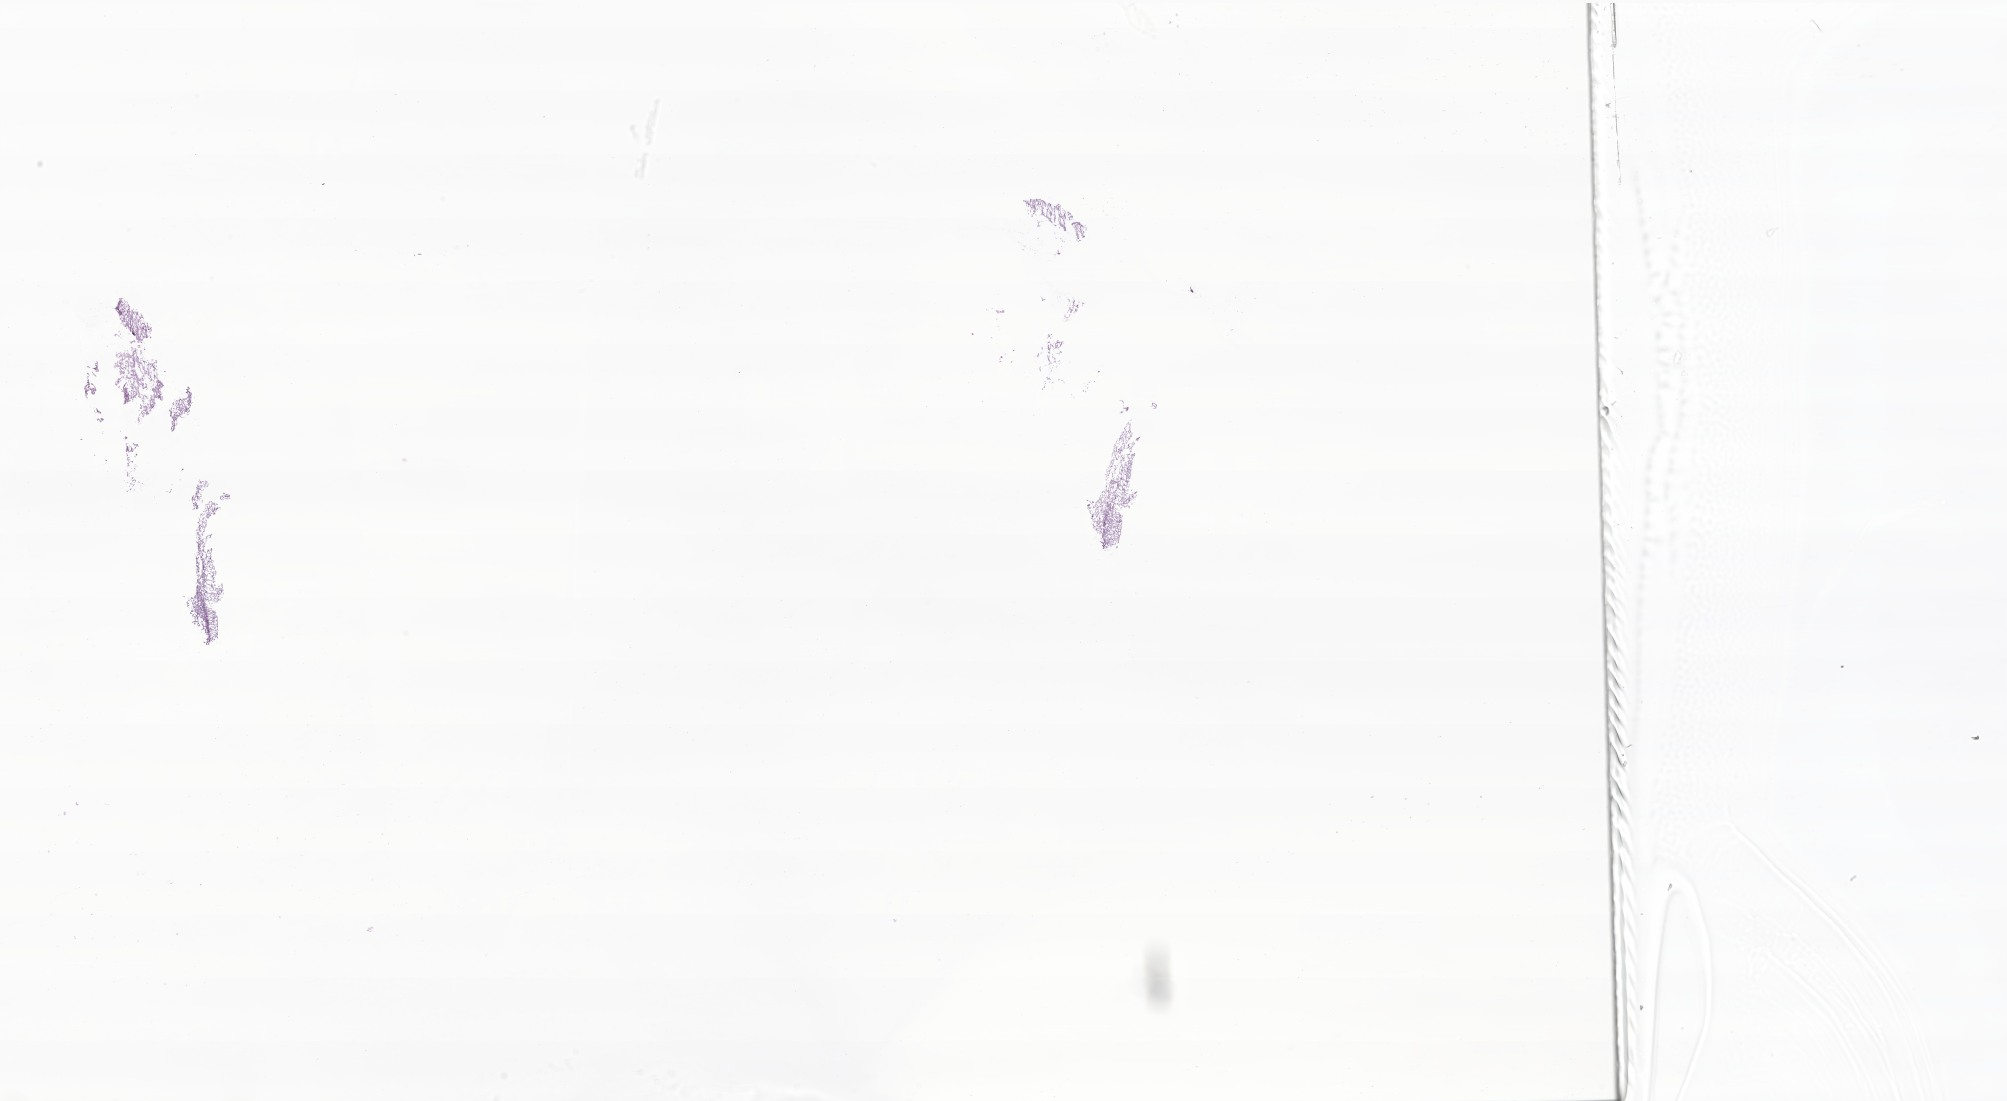
Haematoxylin and eosin whole-slide image of tumor tissue from the frontal lobe — whole scanned area (about 33.8 x 18.6 mm) shown as a low-resolution overview; frozen section. Patient: female, age 224 months (18 years 8 months).
Diagnosis: Astrocytoma, NOS.